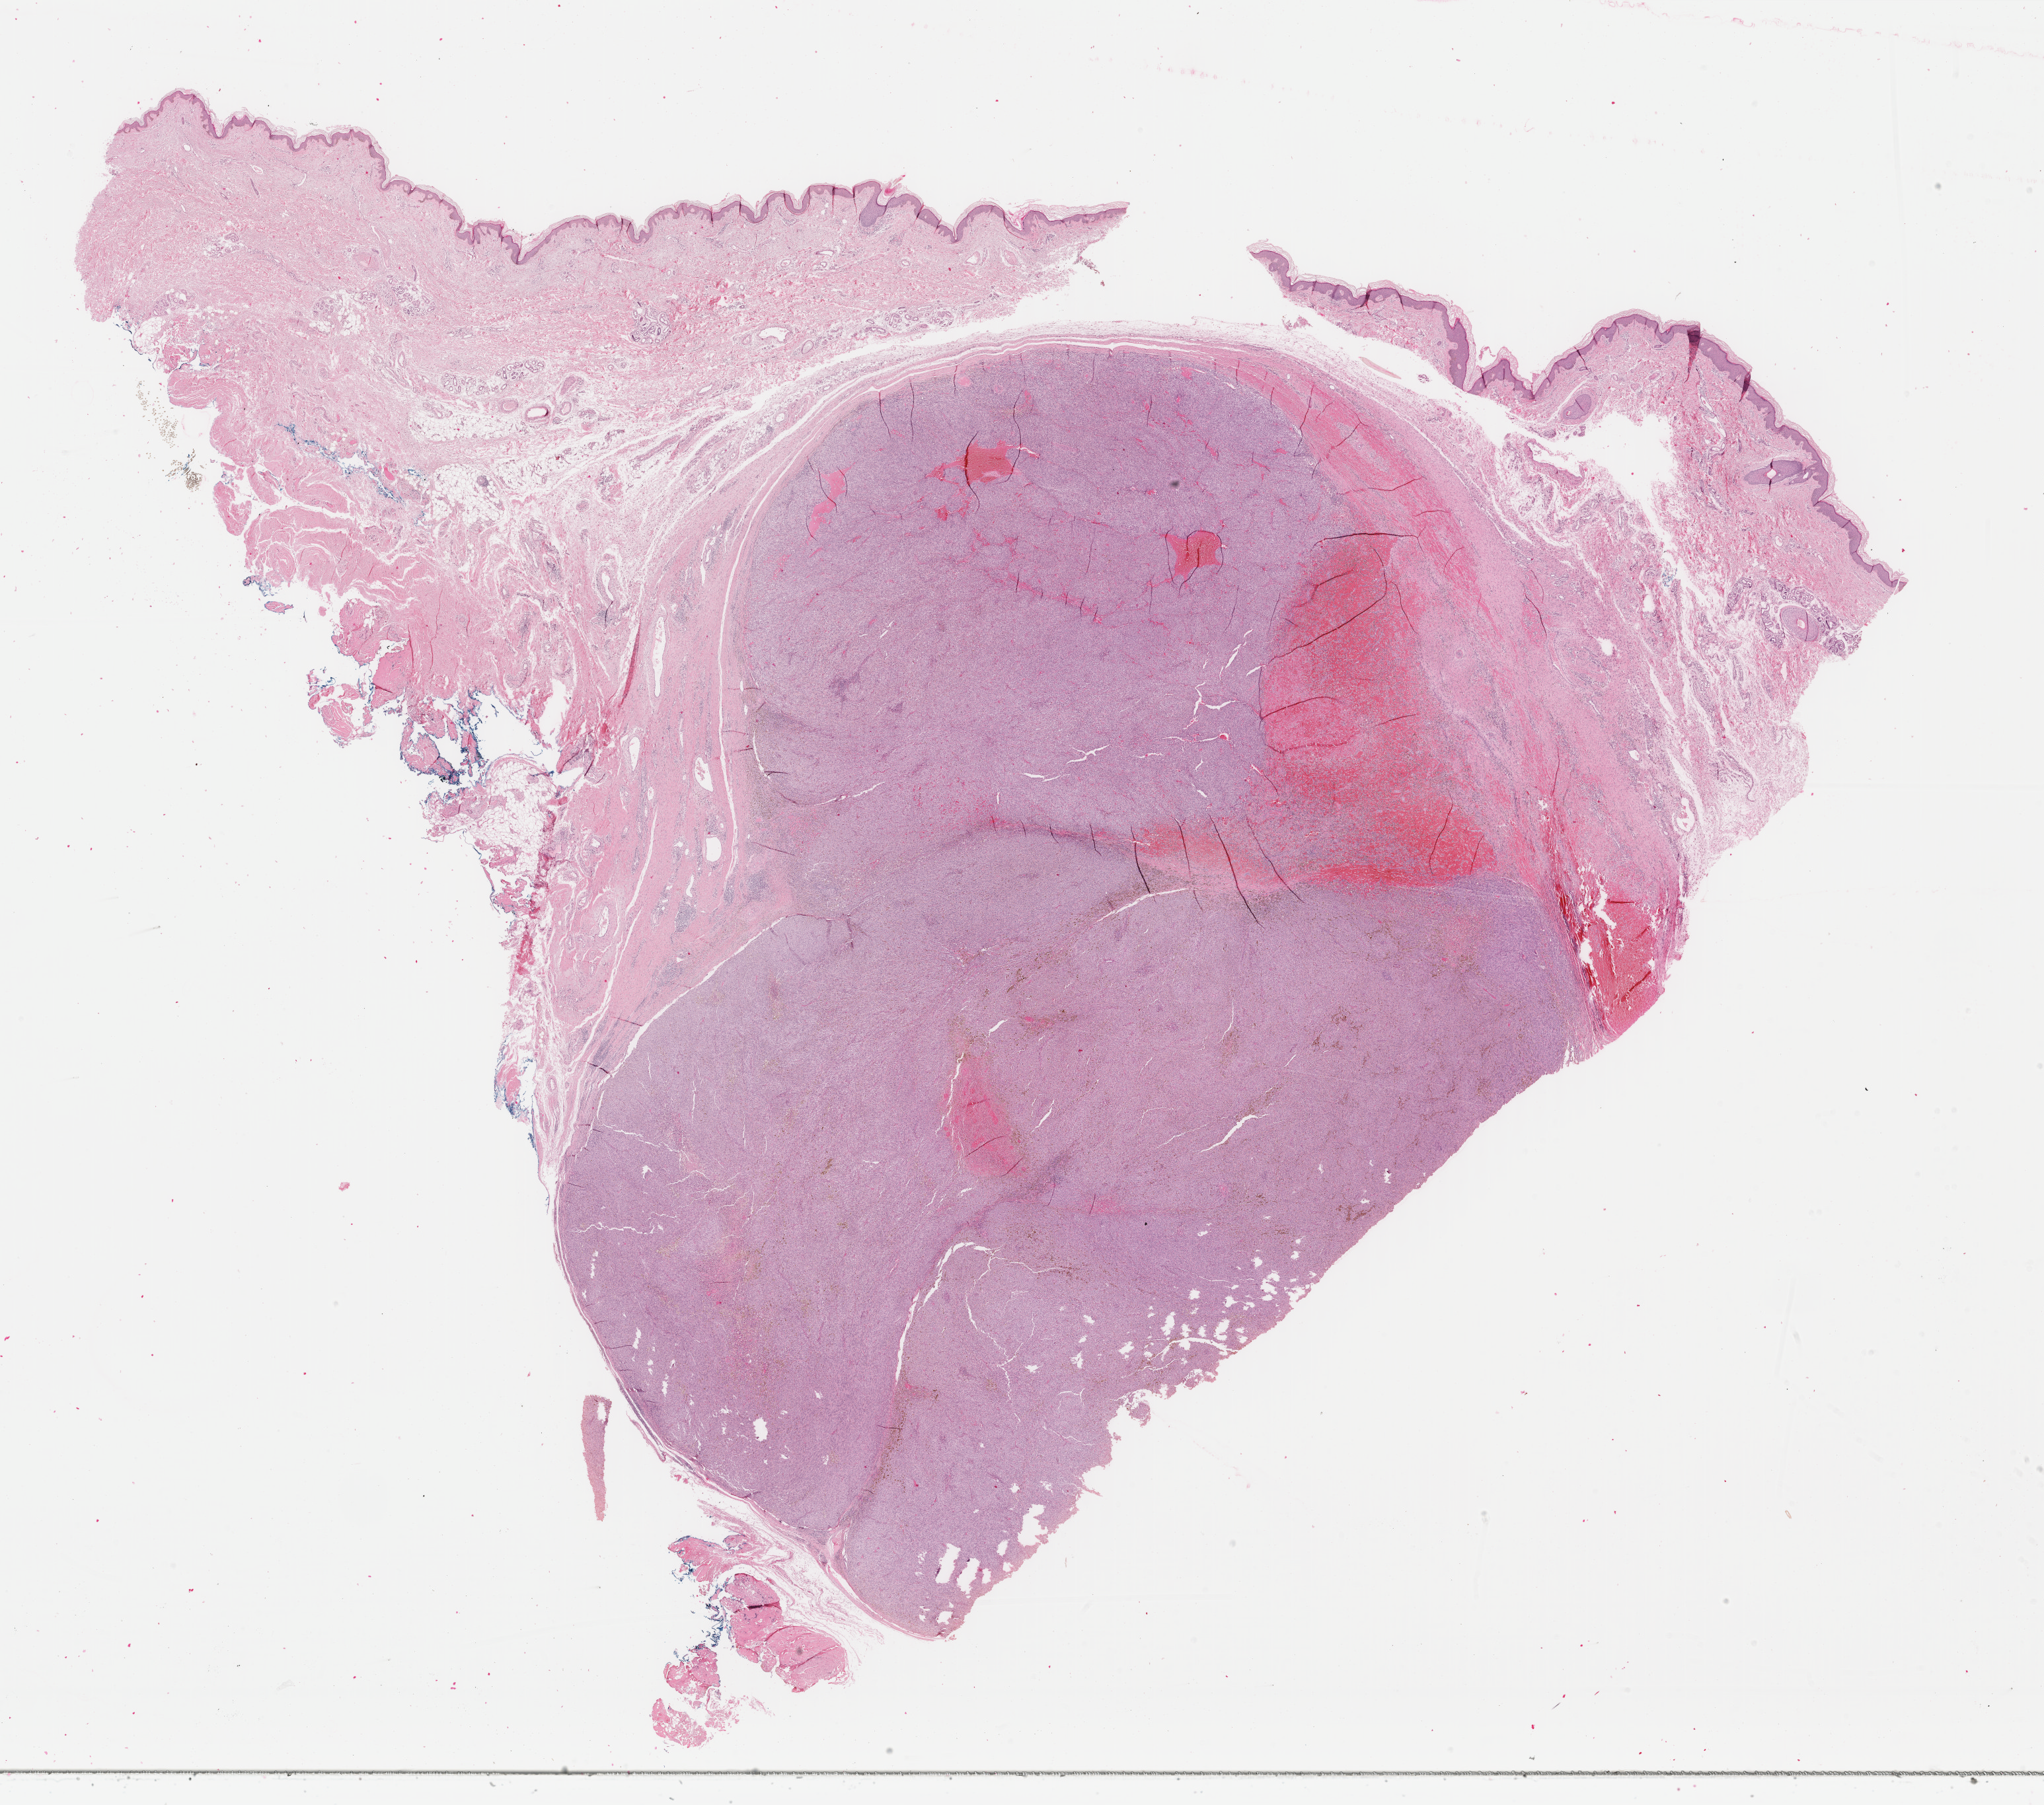
H&E whole-slide image — a low-resolution overview of the entire scanned area, about 24.6 x 21.7 mm (acquisition: 40x scan). Formalin-fixed paraffin-embedded (FFPE) diagnostic section. Sample: primary tumour, skin. Patient: male, age at initial diagnosis 72 years.
Histologic diagnosis: Malignant melanoma, NOS.